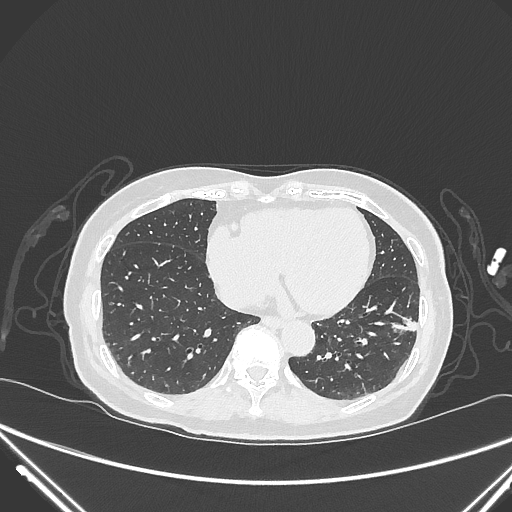
Chest CT, one axial slice. Reconstruction kernel IMR1,SharpPlus. Lung window (W 1500 / L -600 HU). 1 mm slice thickness. 512 × 512 image matrix, field of view 377 × 377 mm. Patient: female, 82 years. Case-level facts recorded for this patient, not image findings: clinical TNM (as recorded): T1c N0 M0.
Annotated regions visible in this slice (bounding box drawn by a radiologist):
- lung tumour (recorded histology: adenocarcinoma): bounding box (x1, y1, x2, y2) in pixels: (387, 310, 422, 342)